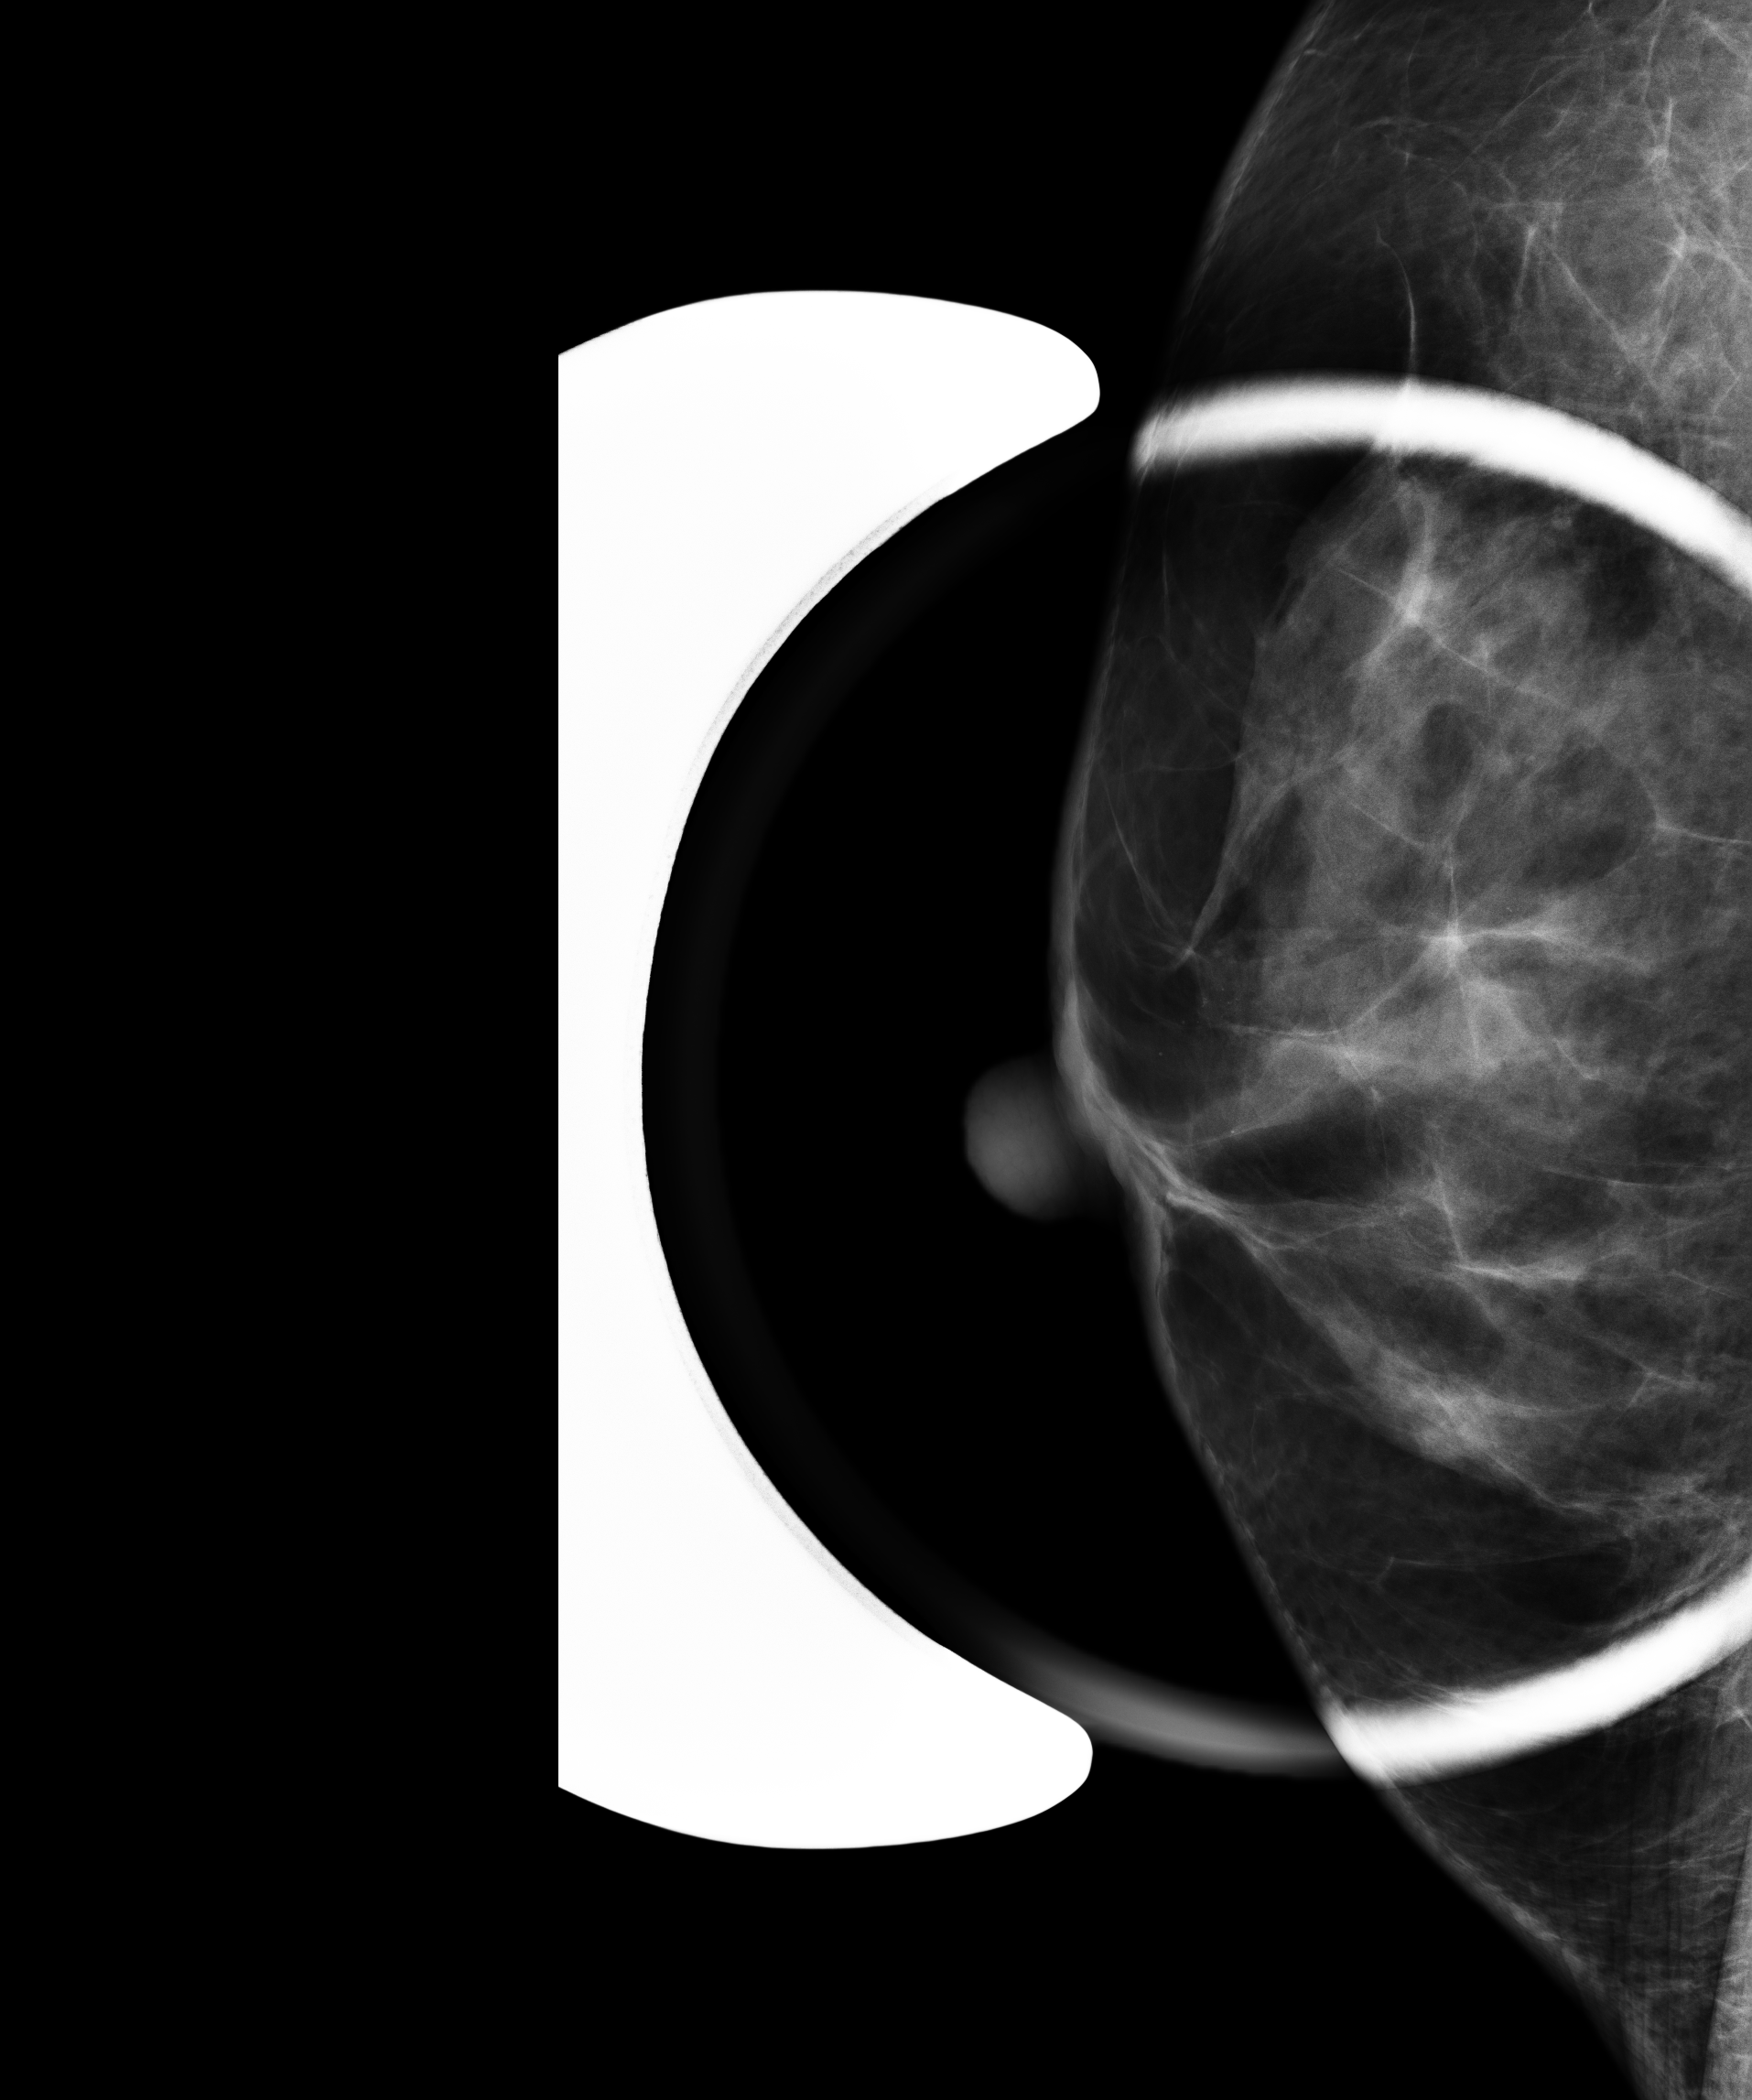
Additional work-up view. Patient aged 58 years (female).
Image type: full-field digital mammogram. Breast: right. Projection: mediolateral (ML) view, spot compression.